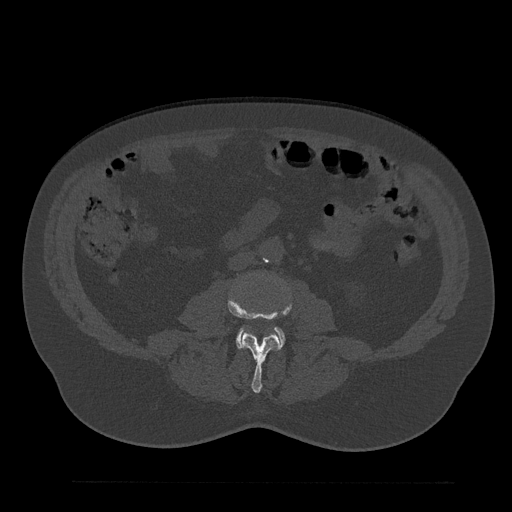
CT including the spine, one axial slice. Slice 8 of 797 in the series (ordered by position). Reconstruction kernel Br40s/3. 120 kVp. Bone window (W 1800 / L 400 HU). 0.5 mm slice thickness. 512 × 512 image matrix, field of view 430 × 430 mm. Patient: male, 61 years. From the clinical record (not read from this slice): primary cancer: prostate.
Annotated regions visible in this slice (semi-automatic segmentation, software-assisted and operator-edited):
- L3 vertebra: bounding box (x1, y1, x2, y2) in pixels: (228, 285, 292, 393)
- L4 vertebra: (236, 328, 285, 347)